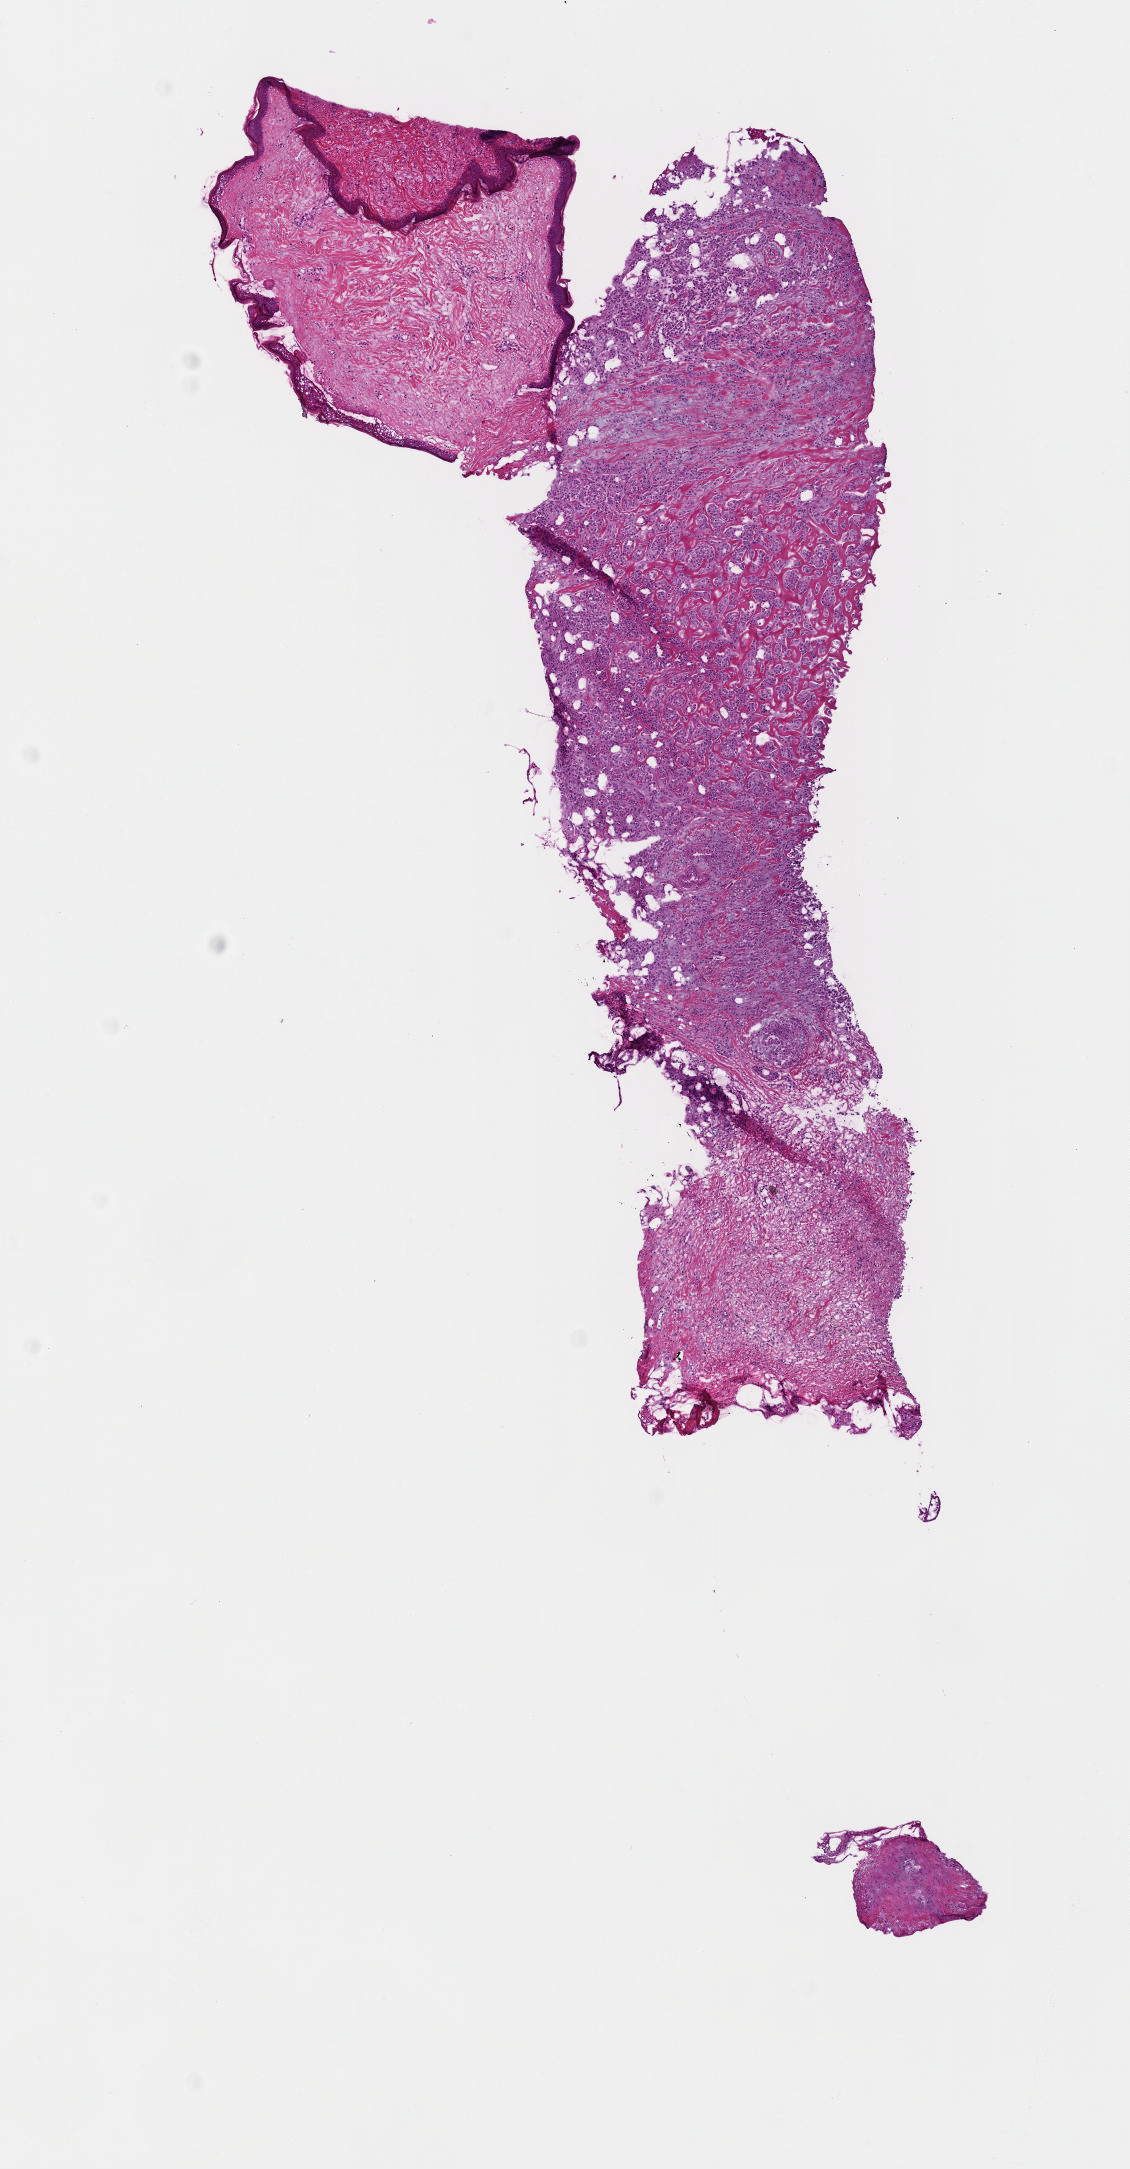
Digitized Hematoxylin and eosin (H&E) stained tissue section (whole slide), low-resolution overview of the scanned area, about 4.5 x 8.6 mm. Frozen section from the top of the tissue portion. Sample: primary tumour, breast. Patient: female, age at initial diagnosis 76 years. Slide review estimates, as recorded: tumour cells 75%, tumour nuclei 75%.
Diagnosis: Lobular carcinoma, NOS.